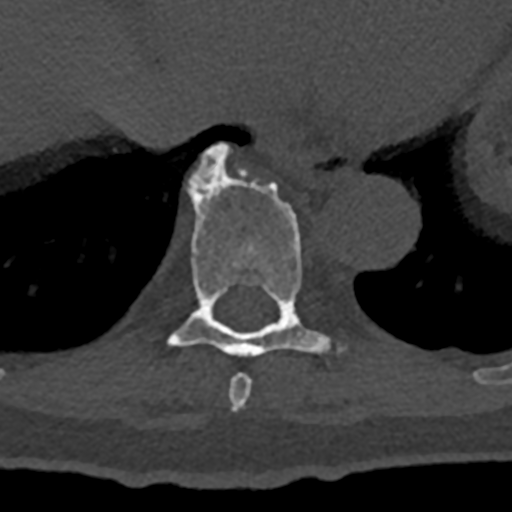
CT including the spine, one axial slice. Position 657 of 797 along the scan axis. Reconstruction kernel Br40s/3. 120 kVp. Bone window (W 1800 / L 400 HU). 0.5 mm slice thickness. 512 × 512 image matrix, field of view 160 × 160 mm. Male patient, age 74 years. From the clinical record (not read from this slice): primary cancer: renal; vertebrae with lytic lesions (as recorded): T10, L1, L2, L3, L4, L5.
Structures marked on this image (semi-automatically segmented with operator editing):
- T10 vertebra: bounding box (x1, y1, x2, y2) in pixels: (212, 145, 221, 149)
- T8 vertebra: (229, 373, 252, 412)
- T9 vertebra: (168, 146, 329, 357)